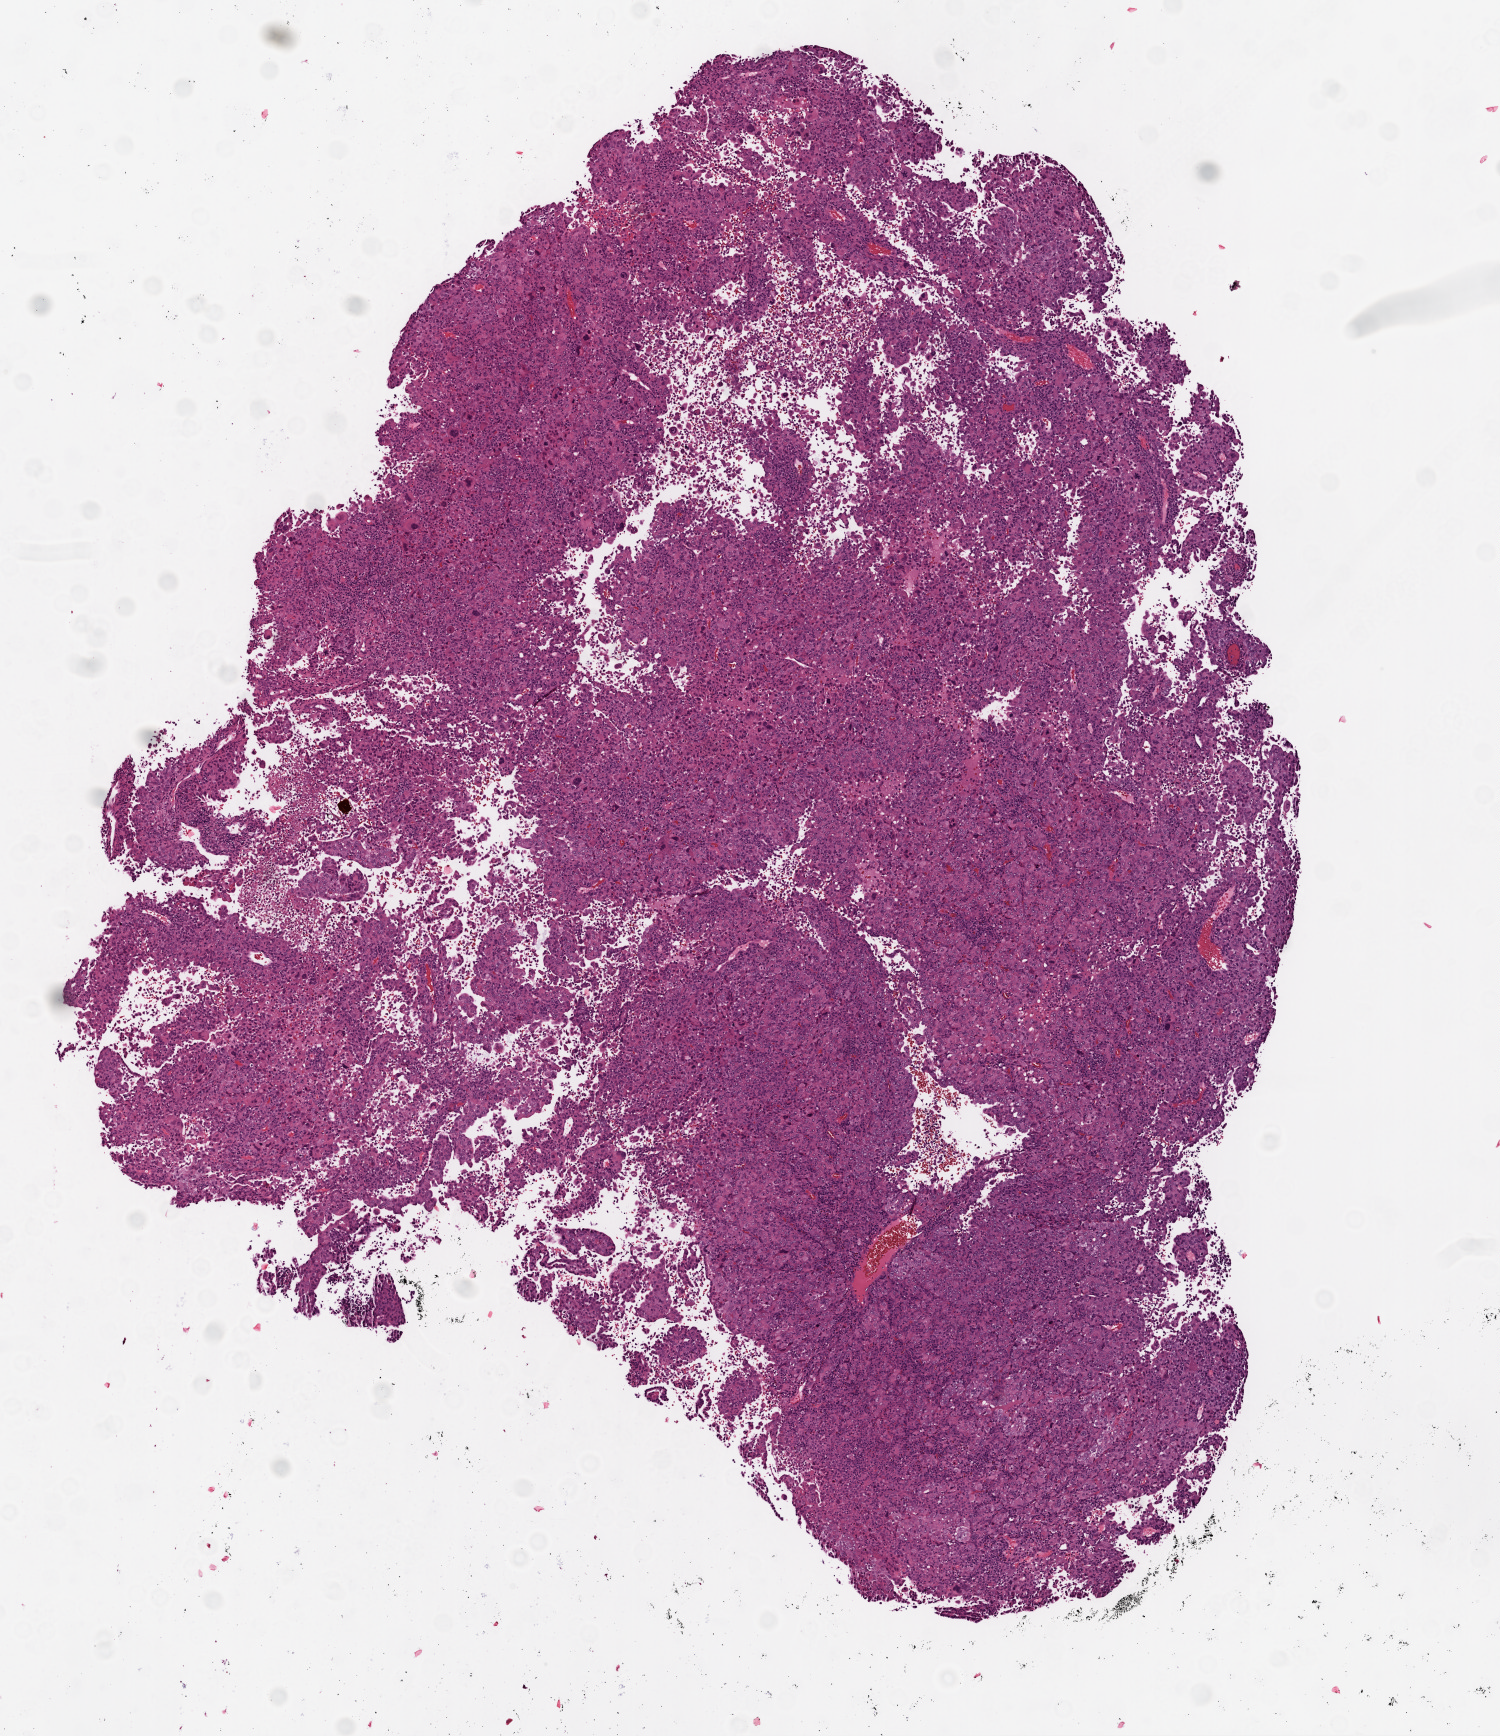
Digitized Hematoxylin and eosin (H&E) stained tissue section (whole slide), a low-resolution overview of the entire scanned area, about 6.0 x 7.0 mm (acquisition: 20x scan); frozen section; lung, primary tumour sample. Patient: female, age at initial diagnosis 47 years. Slide review estimates, as recorded: tumour cells 95%, tumour nuclei 90%.
Histologic diagnosis: Squamous cell carcinoma, NOS (upper lobe, lung).